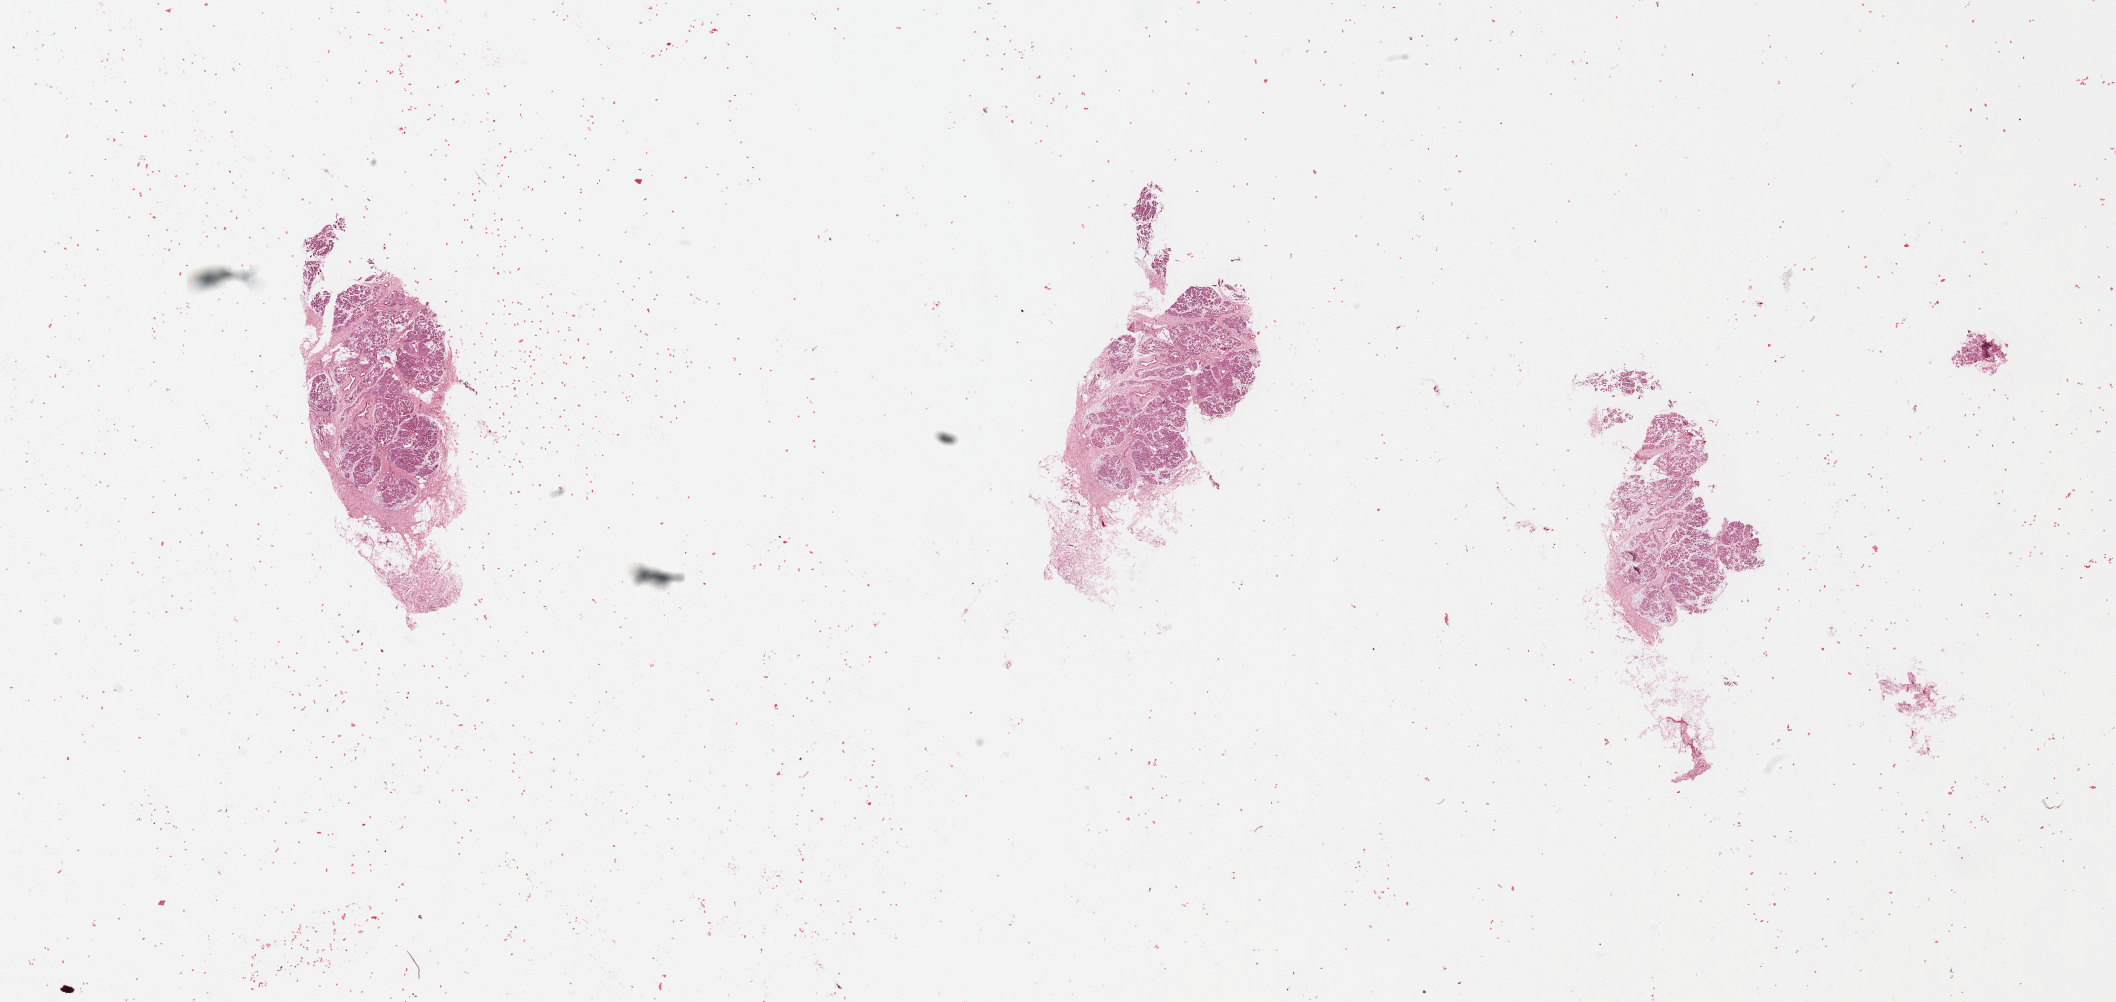
H&E whole-slide image — low-resolution overview of the scanned area, about 33.5 x 15.8 mm (slide scanned at 20x); pancreas, normal (non-tumour) tissue. 53-year-old male patient.
This section: normal (non-tumour) tissue from the same patient. Patient diagnosis (cohort enrolment): ductal adenocarcinoma (pancreas).